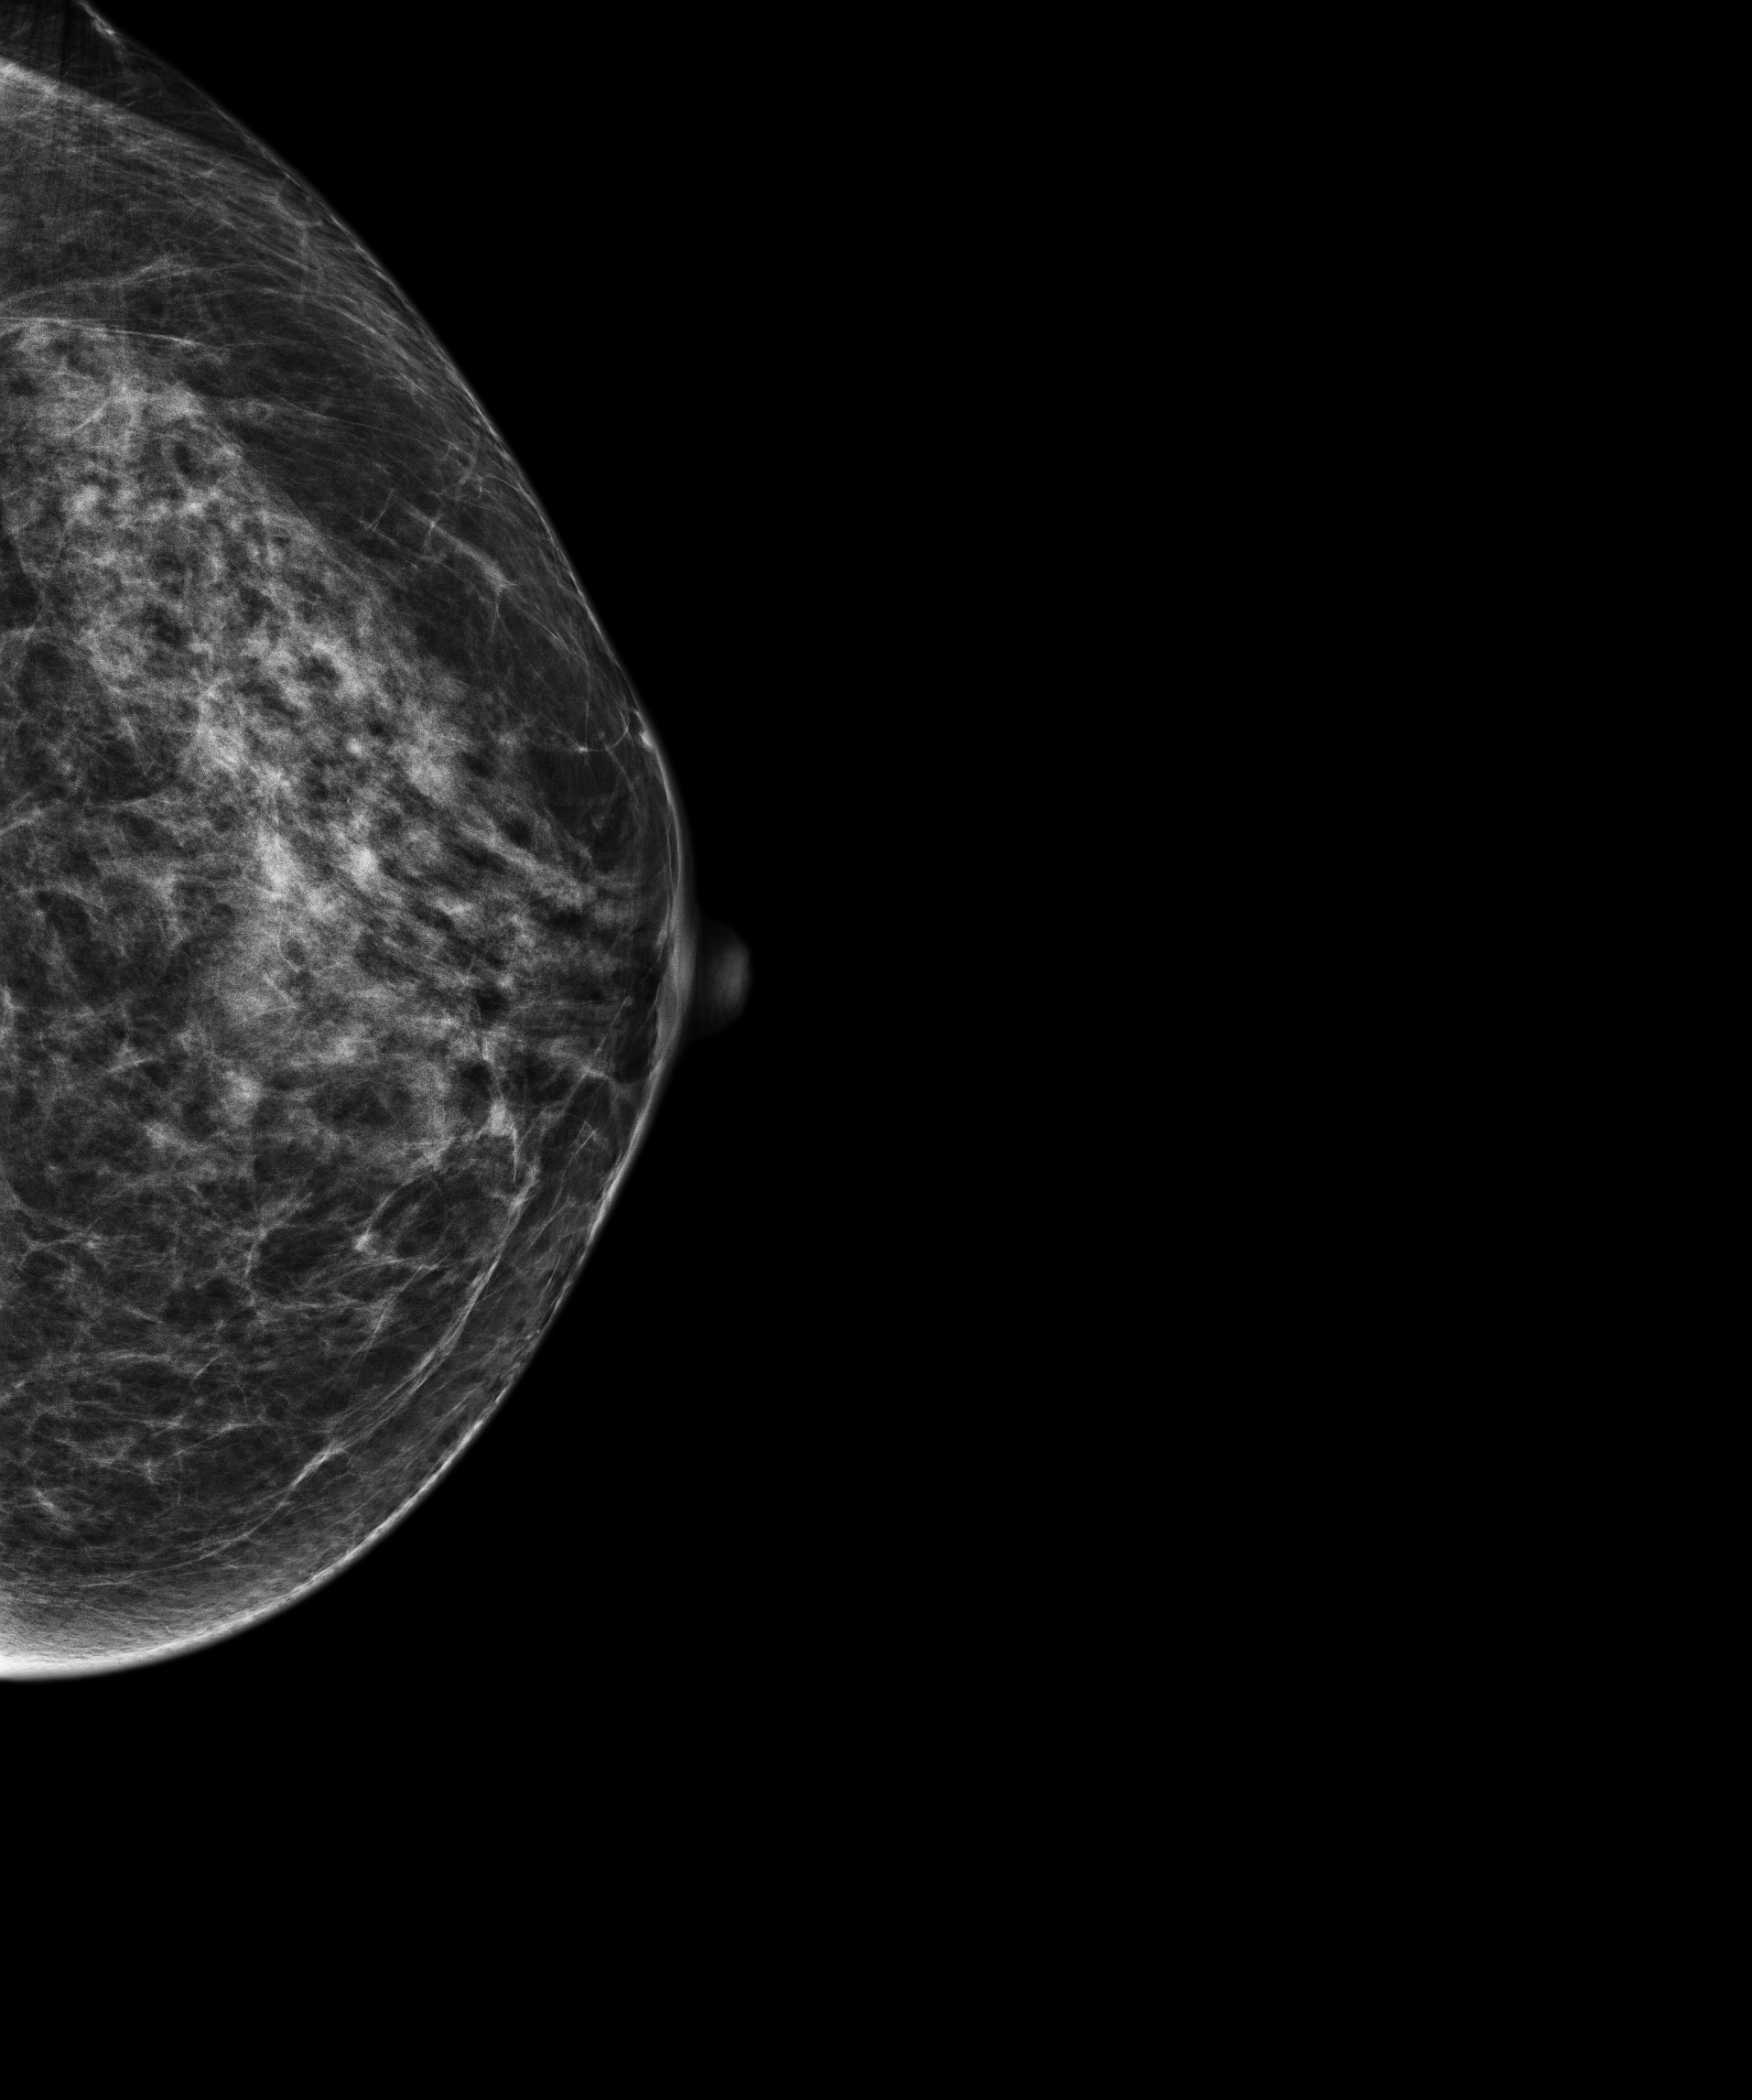
Annual screening mammography examination; compressed breast thickness 61.7 mm. Female patient, age 62 years.
Image type: full-field digital mammogram. Breast: left. Projection: cranio-caudal projection.